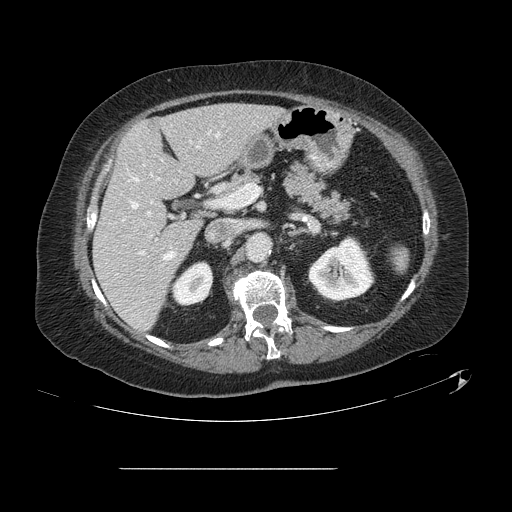
Contrast-enhanced abdominal CT, one axial slice. 120 kVp. Soft-tissue window (W 400 / L 40 HU). 2.5 mm slice thickness. 512 × 512 image matrix. Female patient, age 75 years. Case-level facts recorded for this patient, not image findings: diagnosis: colorectal cancer liver metastases, imaged before liver resection; multiple liver metastases: no; largest metastasis: 2.4 cm.
Annotated regions visible in this slice (outlined manually by an expert reader):
- hepatic veins: box from (x=132, y=134) to (x=219, y=260) px
- liver: (x=94, y=104)–(x=282, y=331)
- planned liver remnant (the part of the liver to remain after resection): (x=94, y=105)–(x=282, y=331)
- portal vein (with intrahepatic branches): (x=138, y=211)–(x=157, y=254)